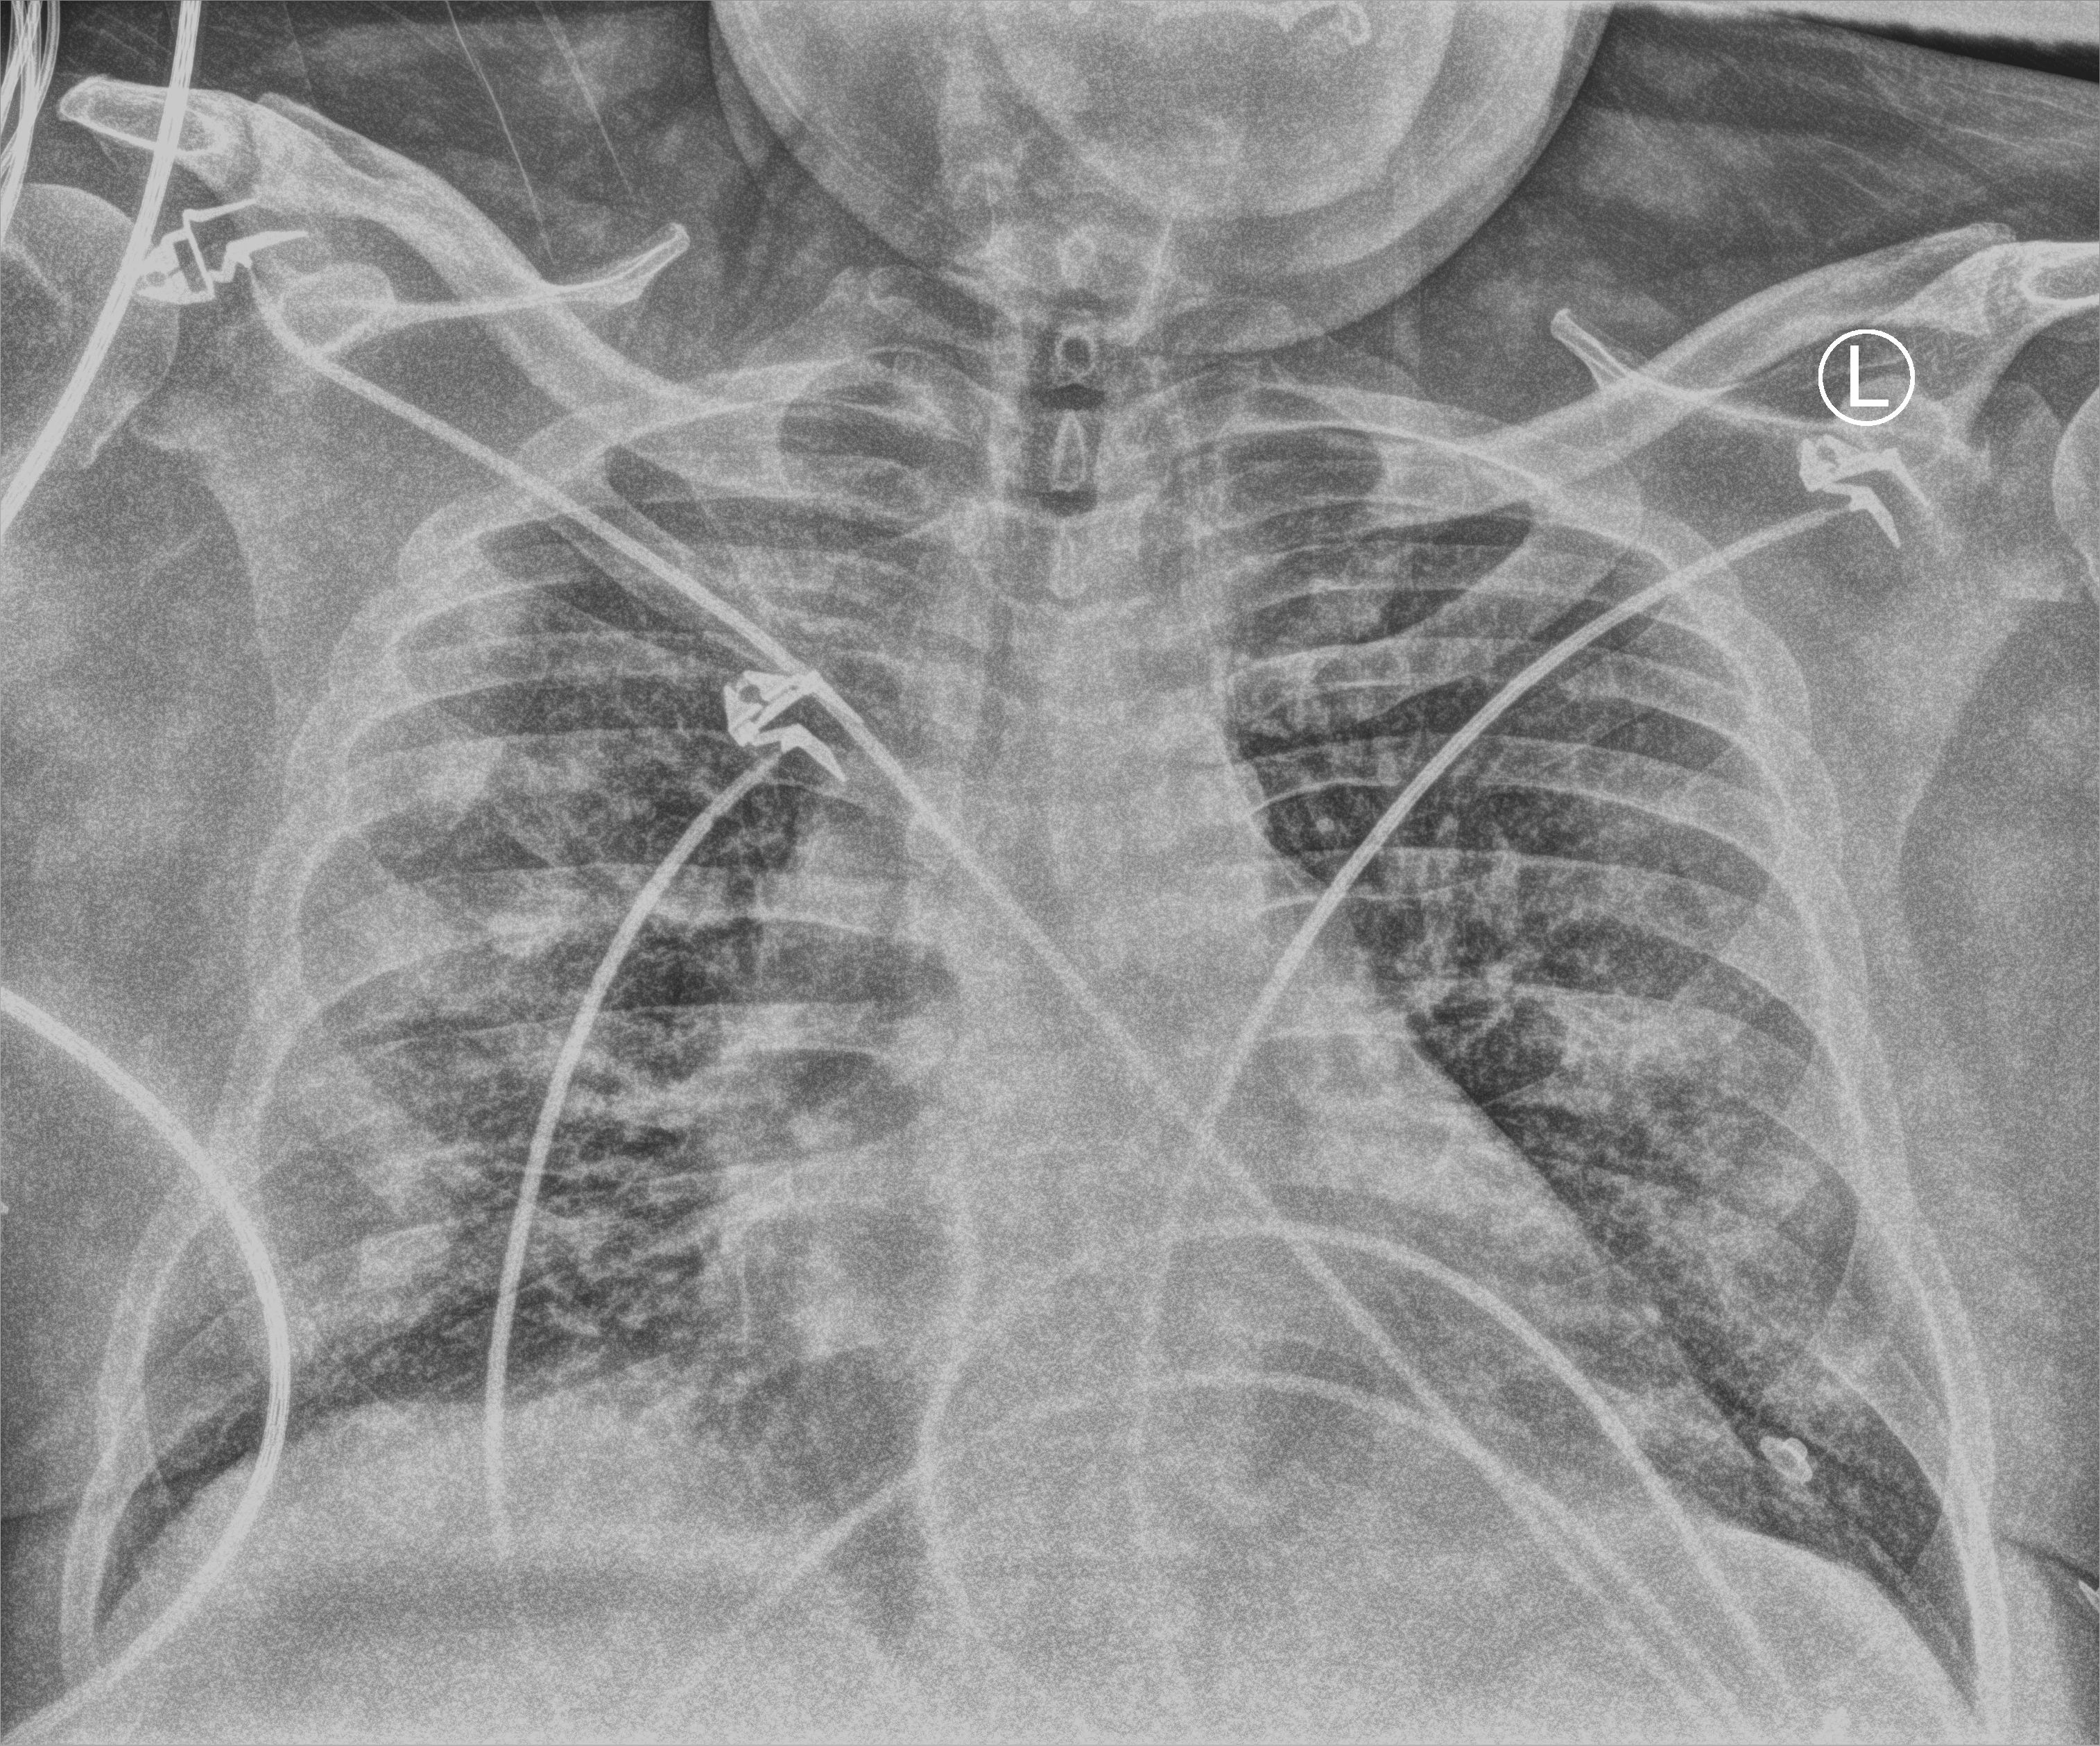
Bedside chest radiograph (computed radiography); anteroposterior (AP) projection. Patient hospitalised with COVID-19; male, aged 60–74 years.
Hospital-stay facts (about this admission, not read from this image; timing relative to this image not recorded): mechanically ventilated during this hospital stay: yes; admitted to intensive care during this hospital stay: yes.